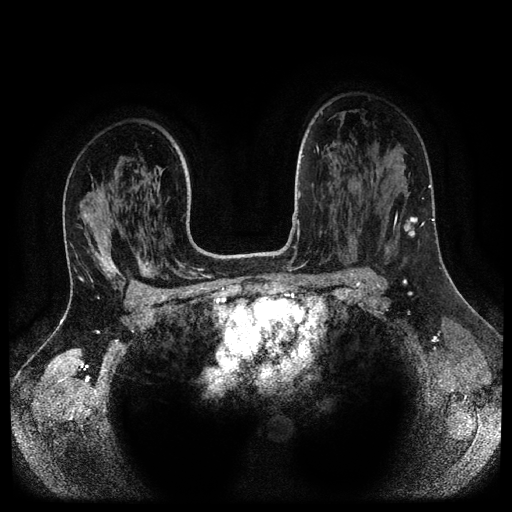
Breast MRI (dynamic contrast-enhanced, multi-phase), one axial slice; slice 71 of 116 in the series (ordered by position); dynamic contrast-enhanced series, time point 2 of 5 at this slice position (early post-contrast); 1.5 T; TE 2.6 ms, TR 5.3 ms; 2.1 mm slice thickness; 512 × 512 image matrix, field of view 360 × 360 mm. Female patient, age 37 years.
Structures marked on this image (semi-automatically segmented with operator editing):
- breast lesion (labelled 'tumour' in the annotation; benign lesions carry a separate 'benign' label): bounding box <404,217,418,238> (left, top, right, bottom; pixels)